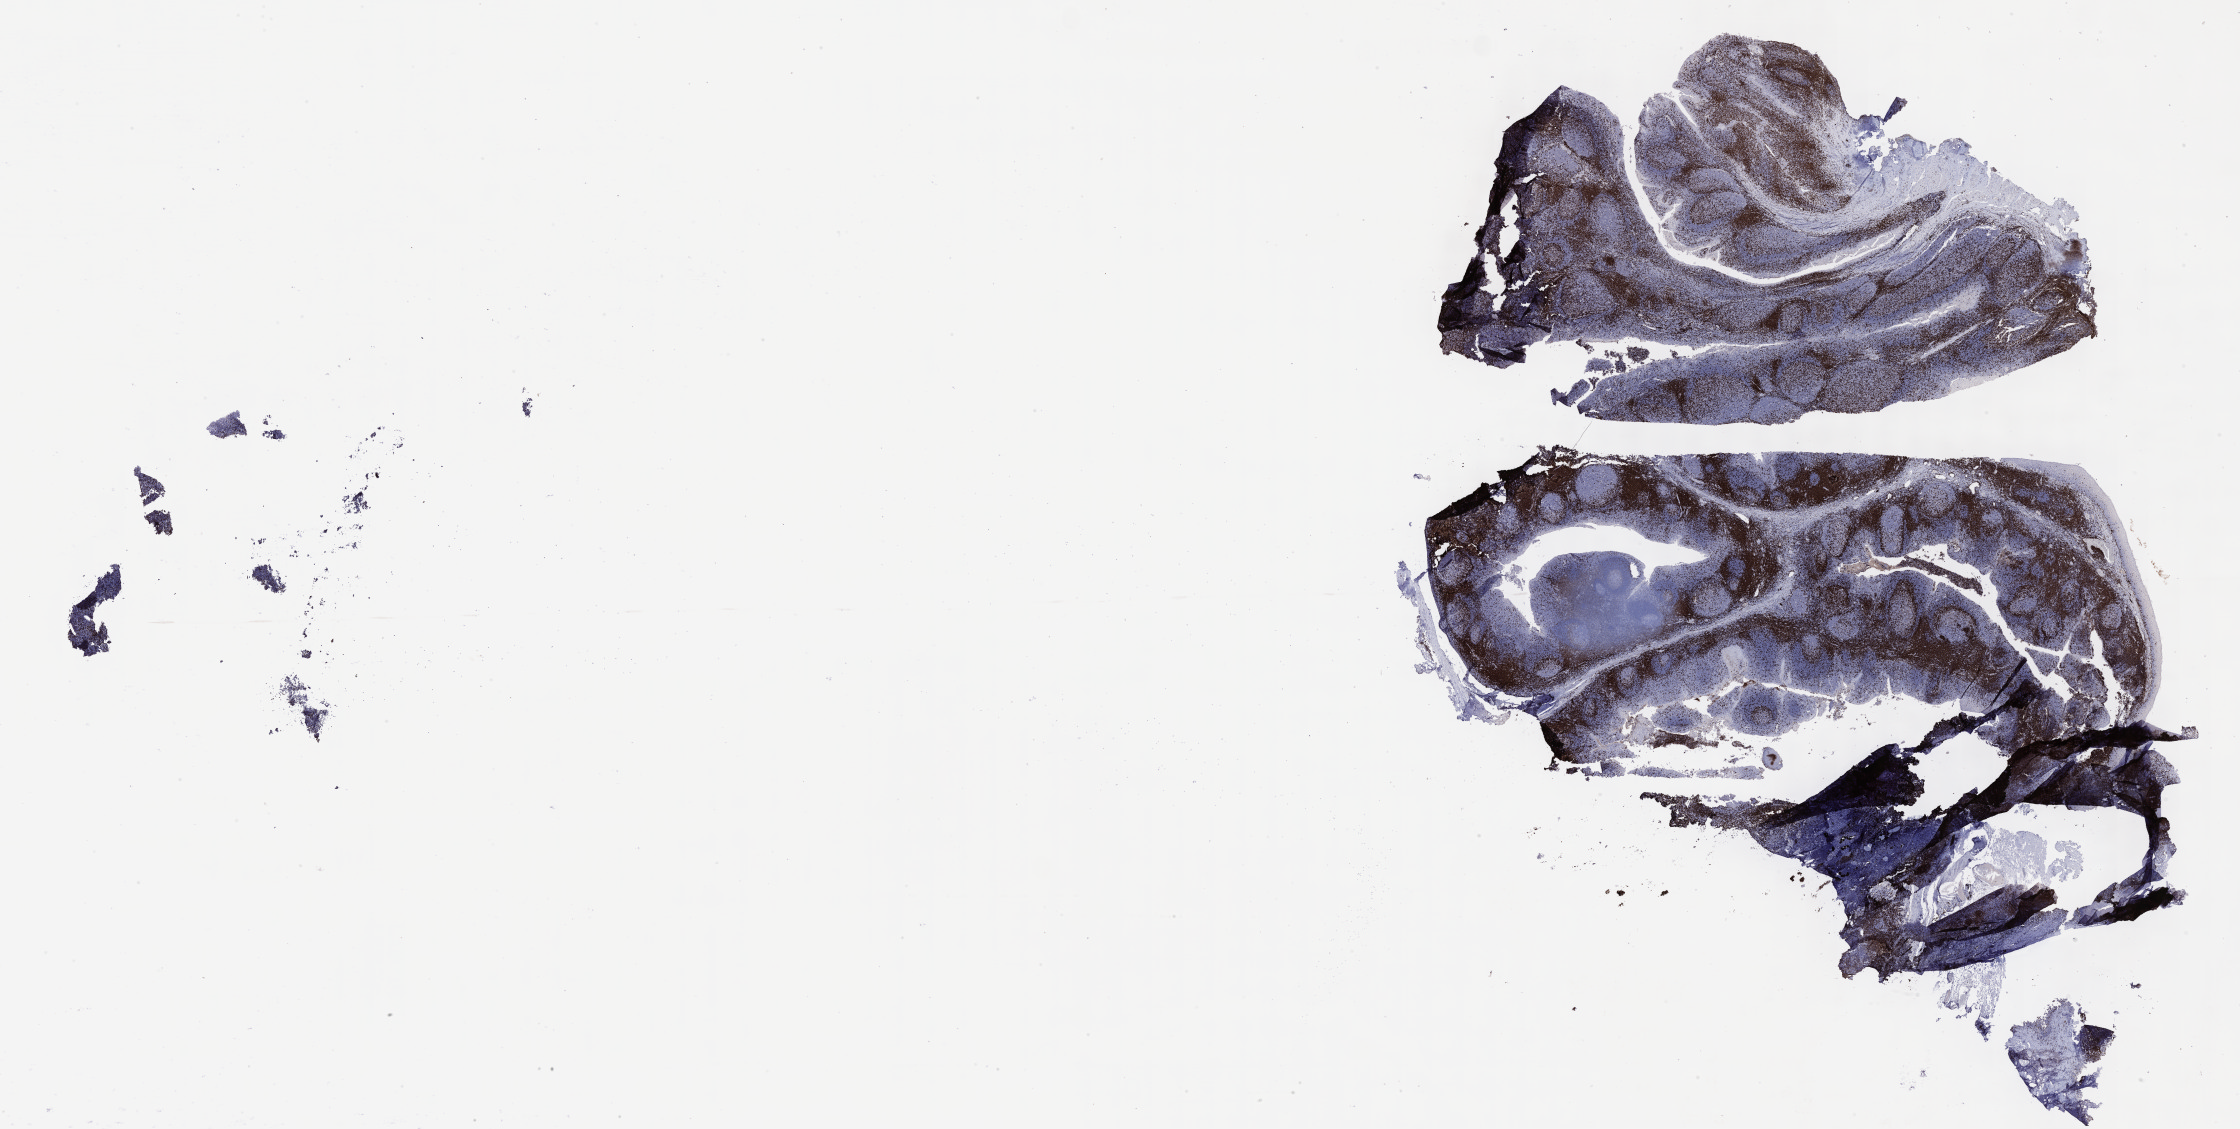
Whole-slide image, immunohistochemical stain for CD3 — shown as a low-resolution overview of the whole scanned area (about 36.2 x 18.3 mm), tumor tissue, site: peritoneum. Female, age 6 years at initial diagnosis.
* diagnosis: Burkitt lymphoma, NOS